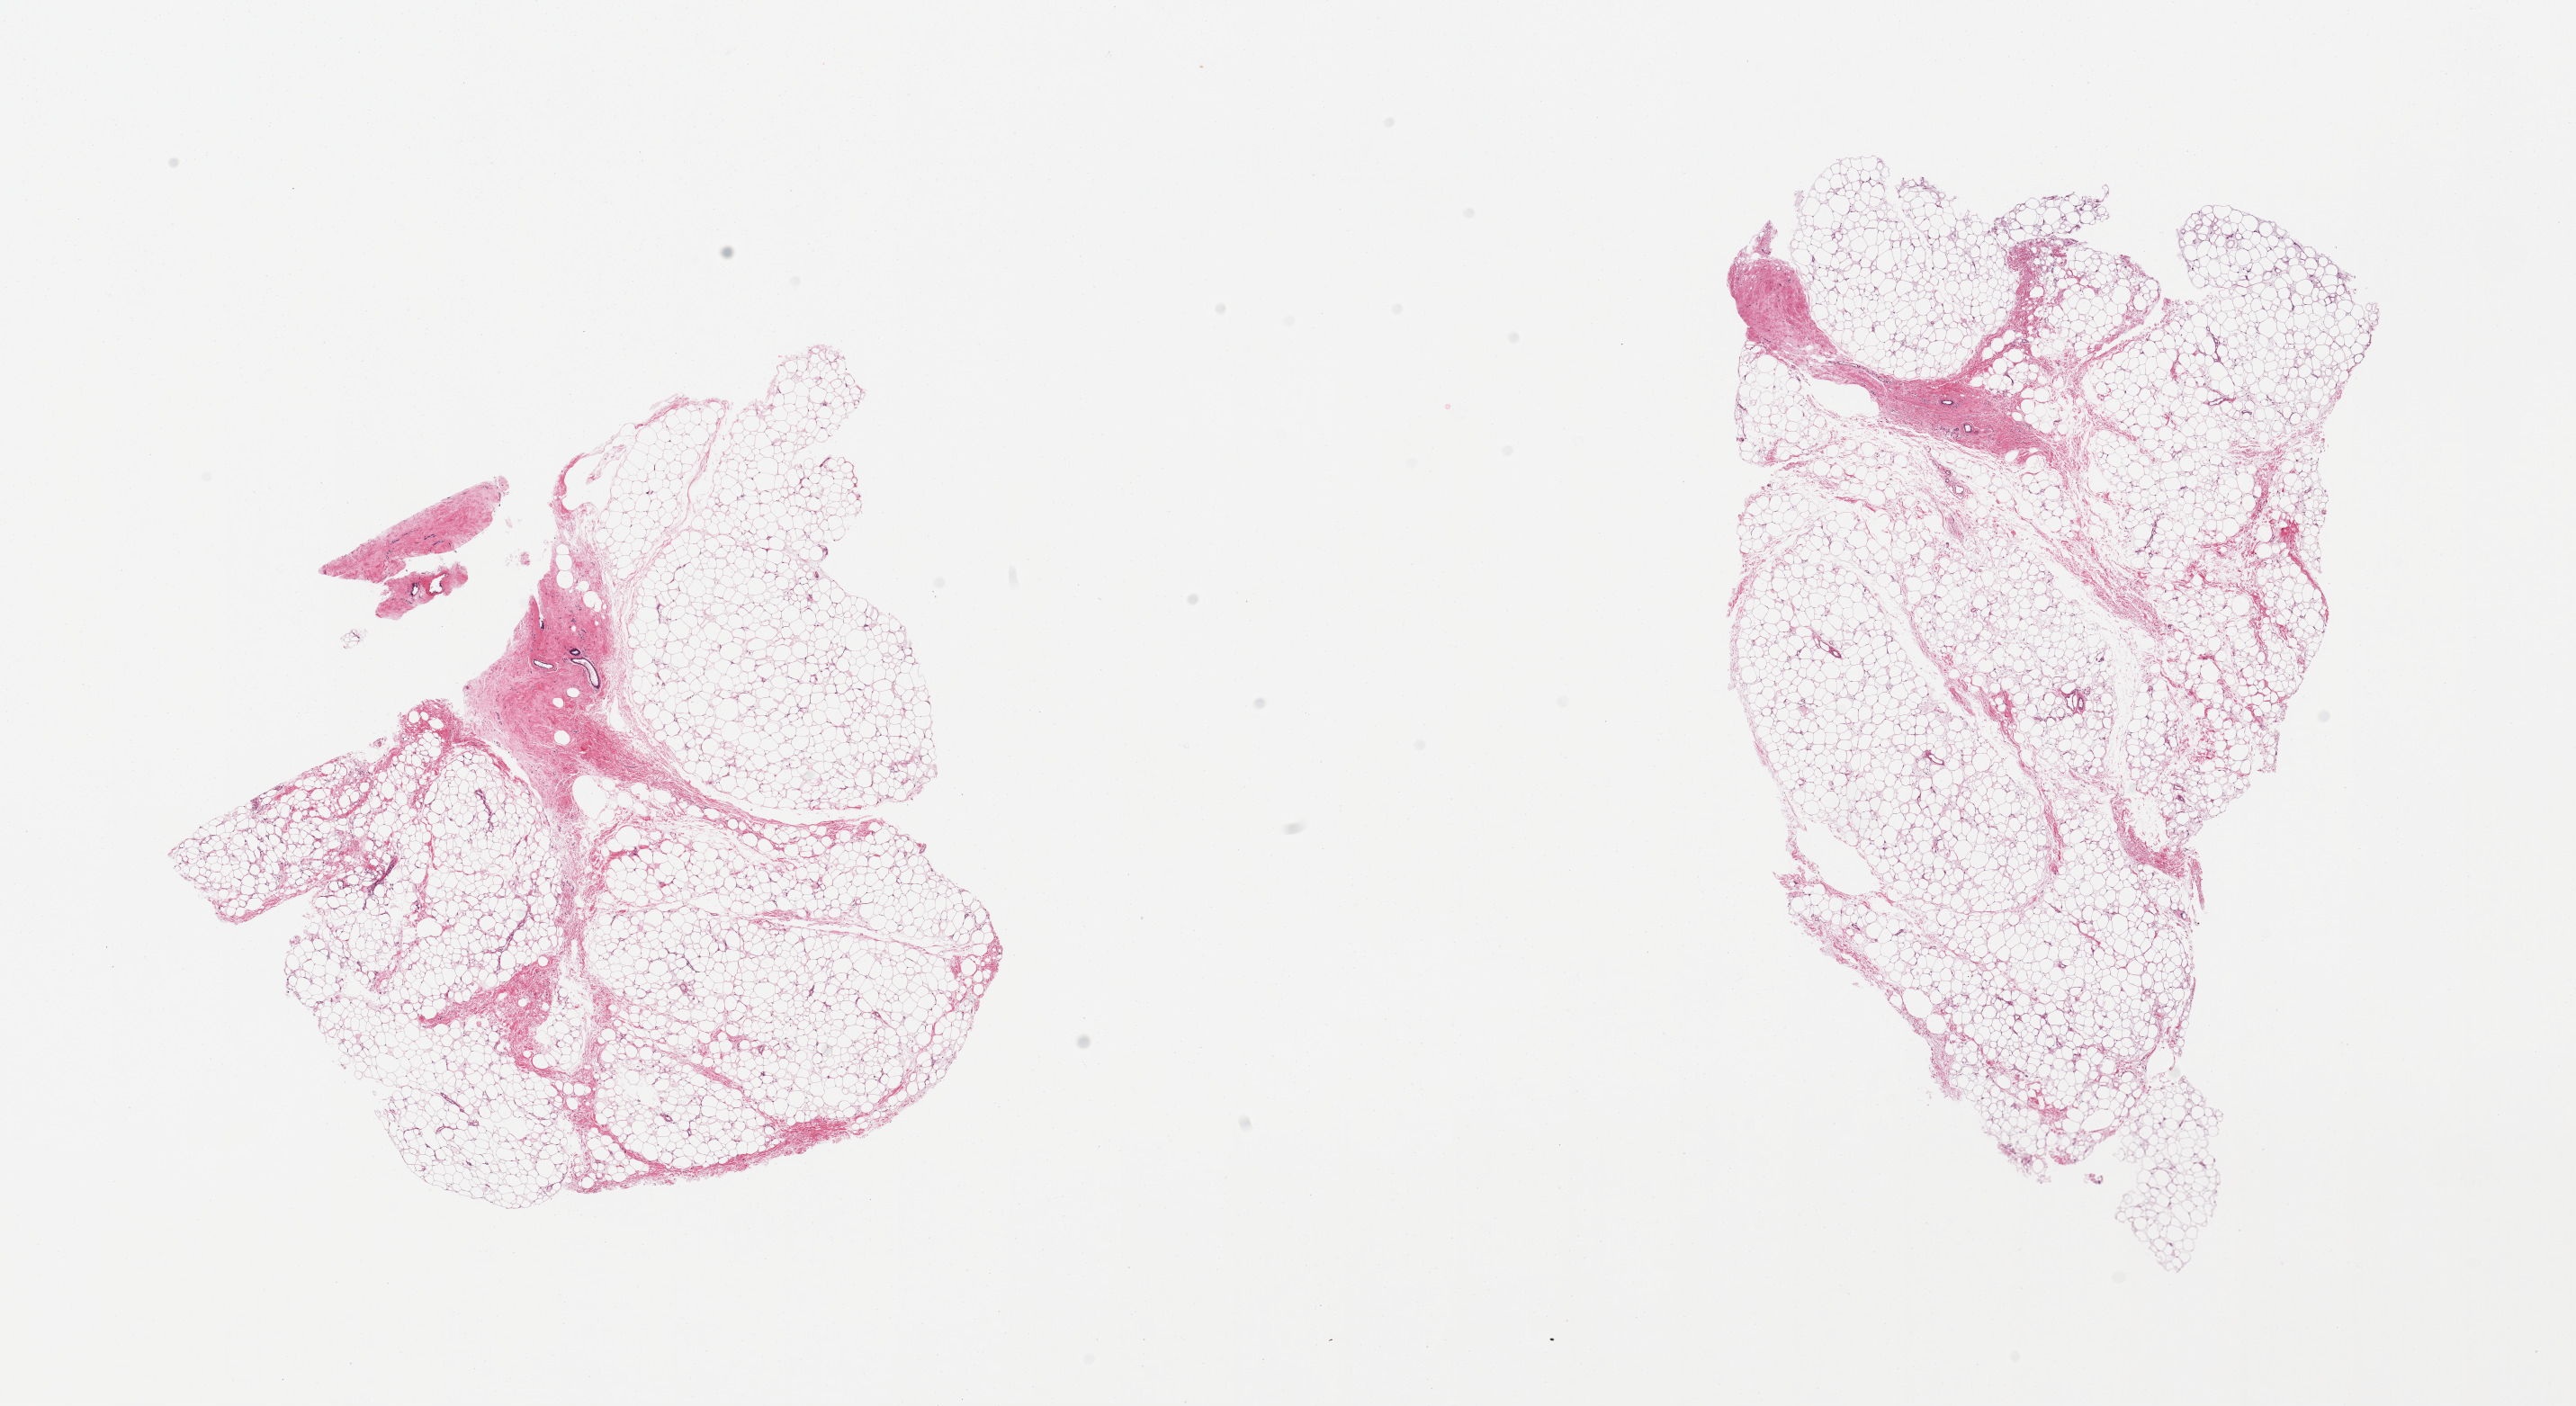
H&E whole-slide image — shown as a low-resolution overview of the whole scanned area (about 22.6 x 12.4 mm); PAXgene-fixed, paraffin-embedded tissue; sampled site (target tissue): breast; tissue donor sample. Donor: male.
* reviewer comment on this tissue sample: 2 pieces, mainly fibroadipose elements, trace ducts